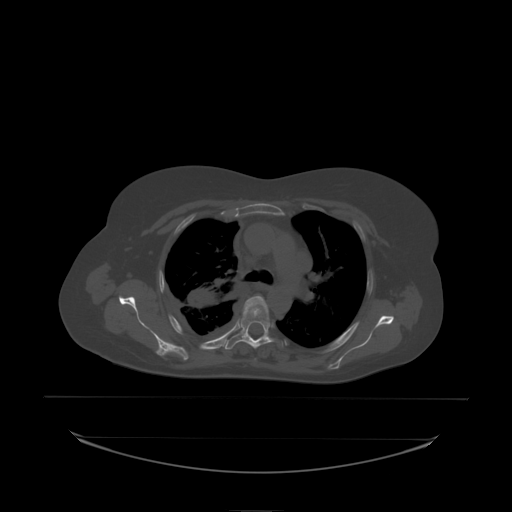
CT including the spine, one axial slice. Slice 160 of 242 in the series (ordered by position). Bone window (W 1800 / L 400 HU). 2.5 mm slice thickness. 512 × 512 image matrix. Patient: female, 53 years. Case-level facts recorded for this patient, not image findings: primary cancer: lung.
Outlined on this slice (semi-automatically segmented with operator editing):
- T4 vertebra: box from (x=243, y=296) to (x=266, y=314) px
- T5 vertebra: (x=238, y=302)–(x=270, y=338)